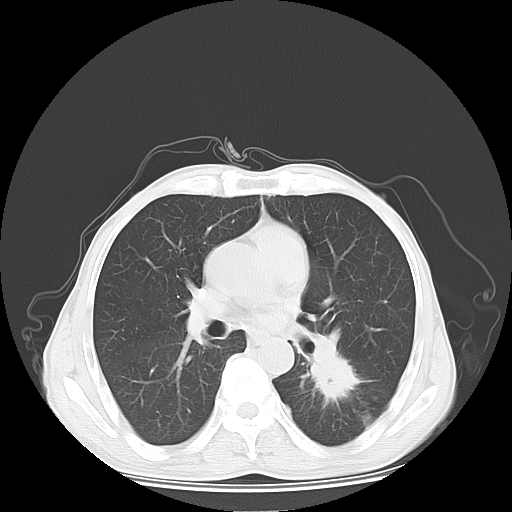
Chest CT, one axial slice; slice 34 of 65 in the series (ordered by position); reconstruction kernel LUNG; 120 kVp; lung window (W 1500 / L -600 HU); 5 mm slice thickness; 512 × 512 image matrix, field of view 350 × 350 mm. Male patient, age 63 years. Case-level facts recorded for this patient, not image findings: clinical TNM (as recorded): T1c N0 M1b.
Structures marked on this image (bounding box drawn by a radiologist):
- lung tumour (recorded histology: adenocarcinoma): box from (x=301, y=332) to (x=366, y=406) px